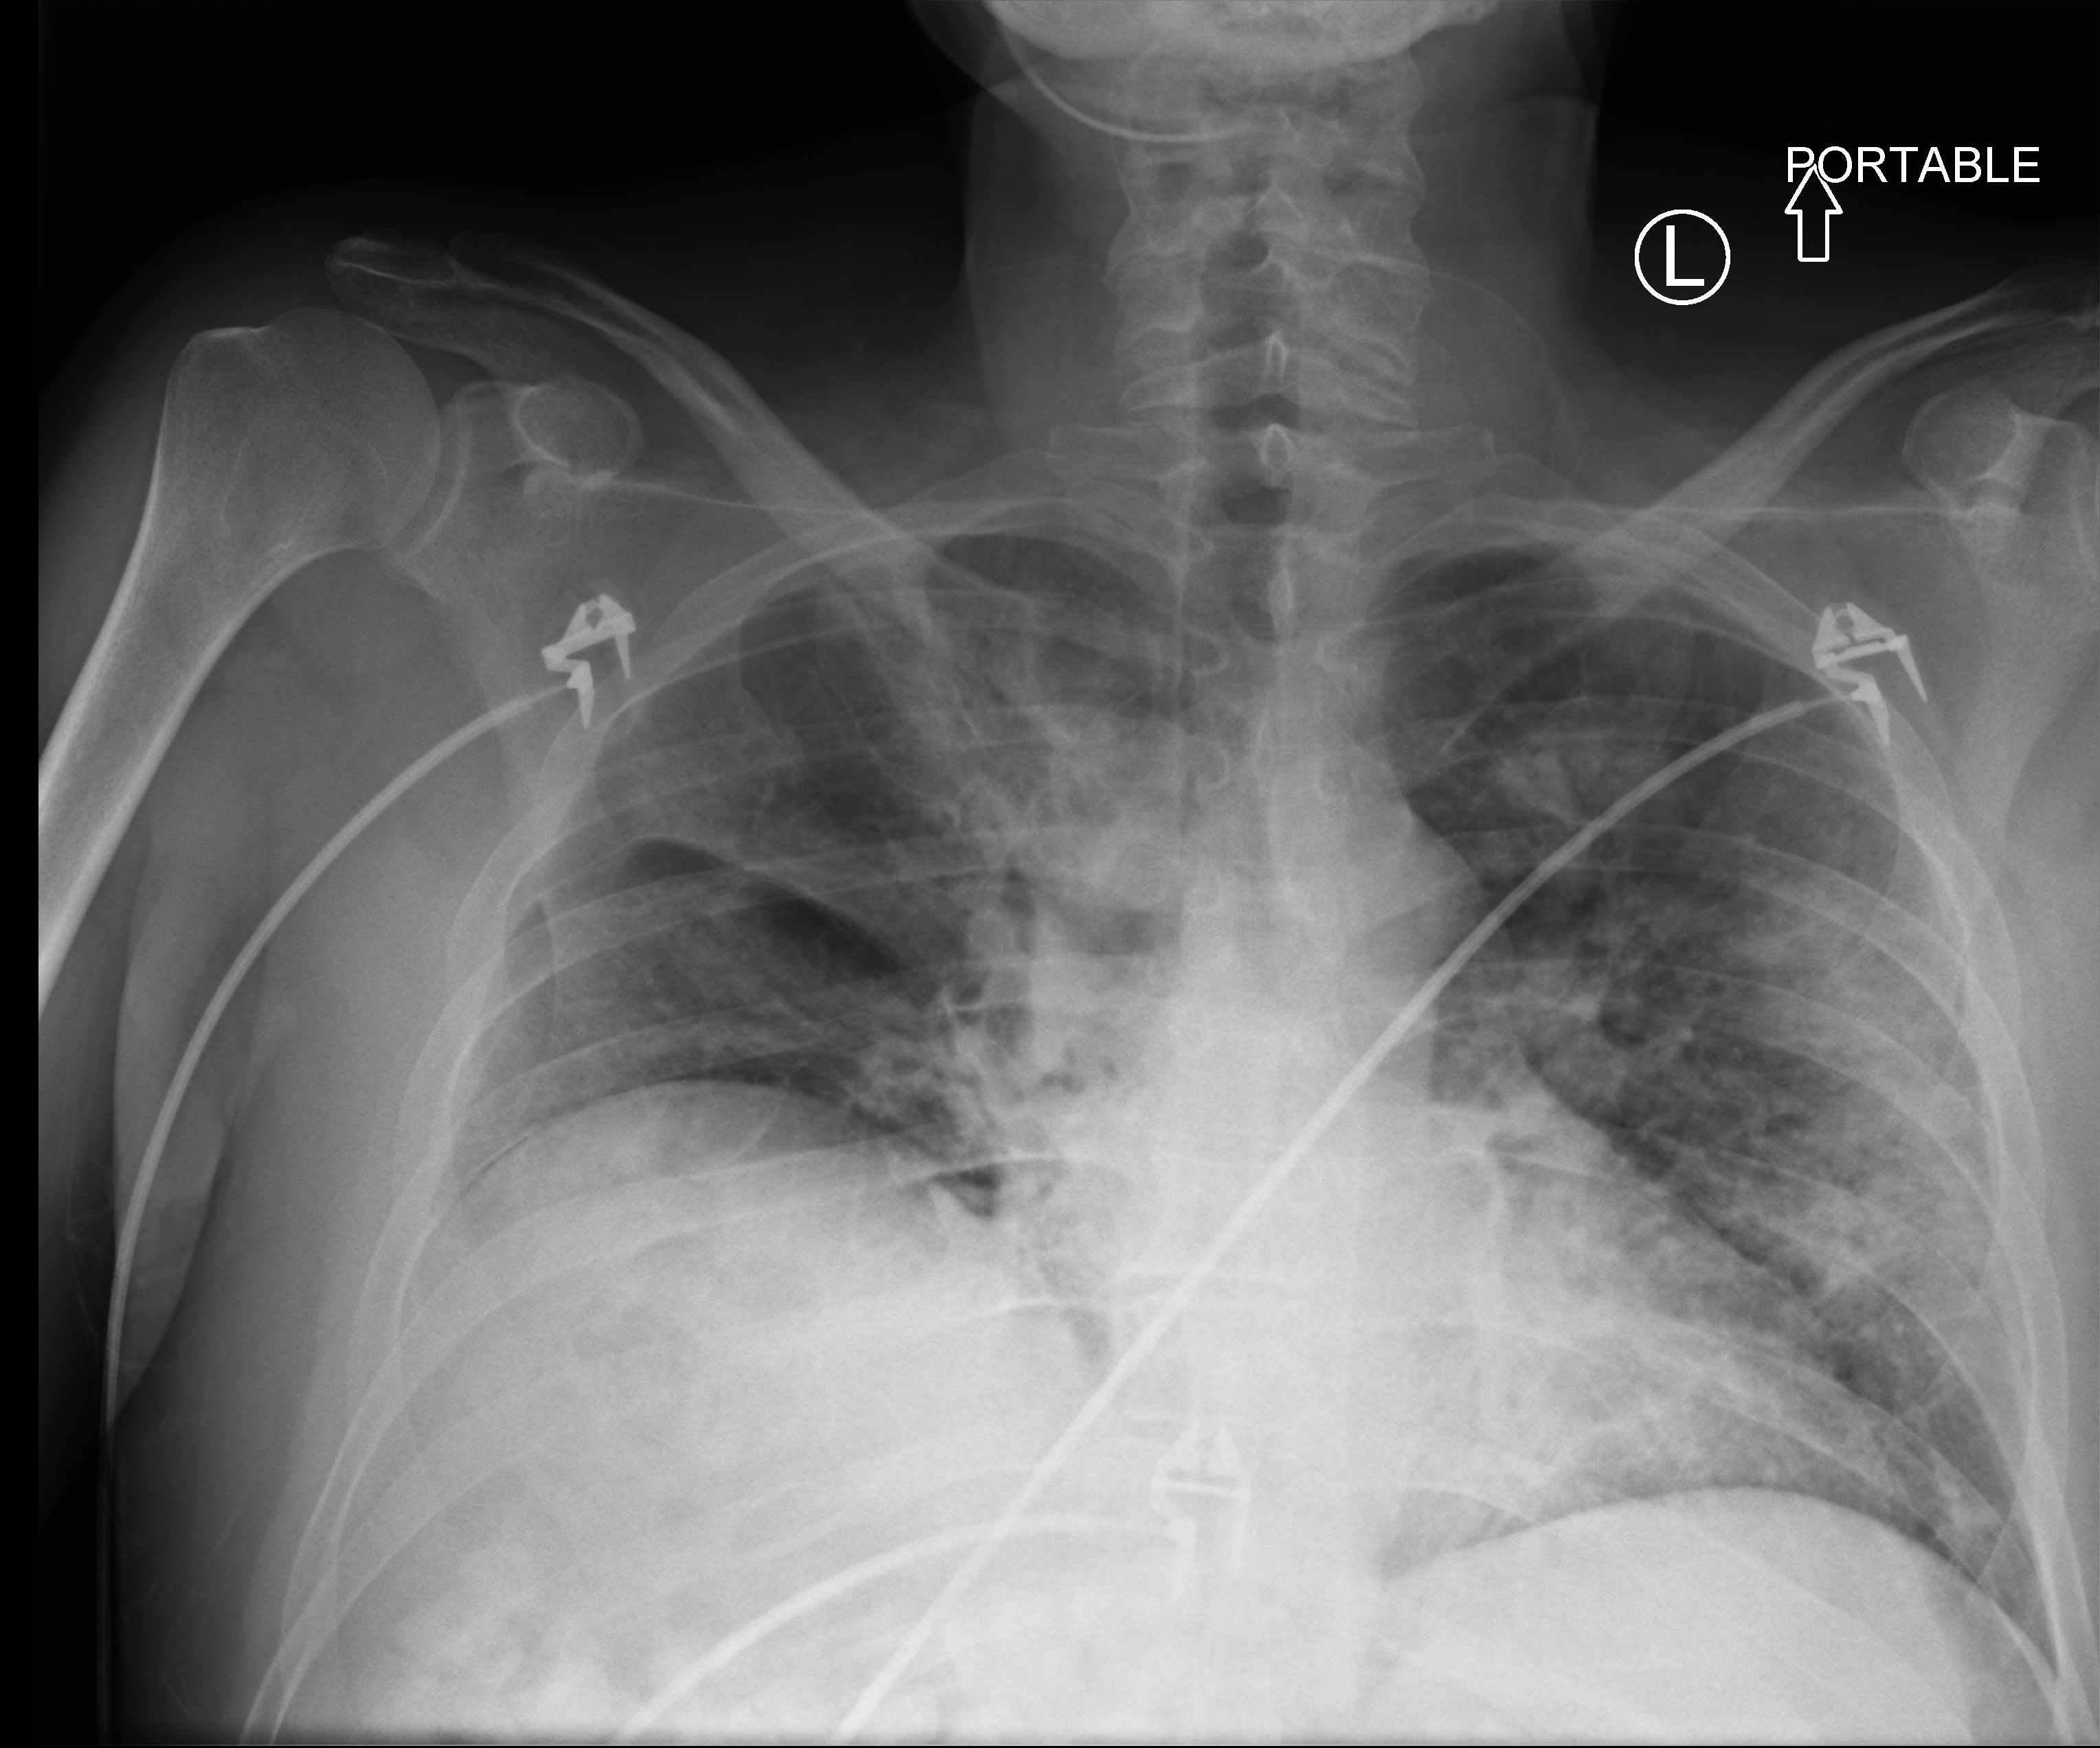
Chest X-ray (portable), anteroposterior (AP) projection. Male patient hospitalised with COVID-19, age 18–59 years.
From the hospital-stay record, not from the radiograph (when in the stay this image was taken is not recorded): mechanically ventilated during this hospital stay: yes; length of hospital stay: 48 days; admitted to intensive care during this hospital stay: yes.